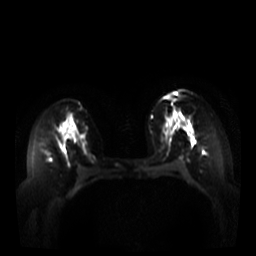
Breast MRI, one axial slice. Position 21 of 44 along the scan axis. Diffusion-weighted series; image 2 of 4 stored at this slice position (different b-values; order by instance number). 3 T. 5 mm slice thickness. 256 × 256 image matrix. Female patient.
Structures marked on this image (manually delineated by an expert):
- tumour on diffusion-weighted imaging: bounding box (x1, y1, x2, y2) in pixels: (189, 130, 193, 137)